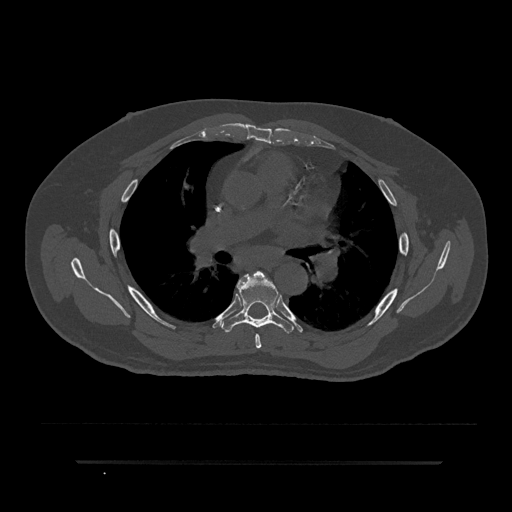
CT including the spine, one axial slice; 120 kVp; bone window (W 1800 / L 400 HU); 0.5 mm slice thickness; 512 × 512 image matrix, field of view 464 × 464 mm. Male patient, age 59 years. From the clinical record (not read from this slice): primary cancer: bile ducts.
Structures marked on this image (semi-automatically segmented with operator editing):
- T5 vertebra: bounding box [x1, y1, x2, y2] px = [253, 272, 264, 349]
- T6 vertebra: [221, 271, 293, 334]